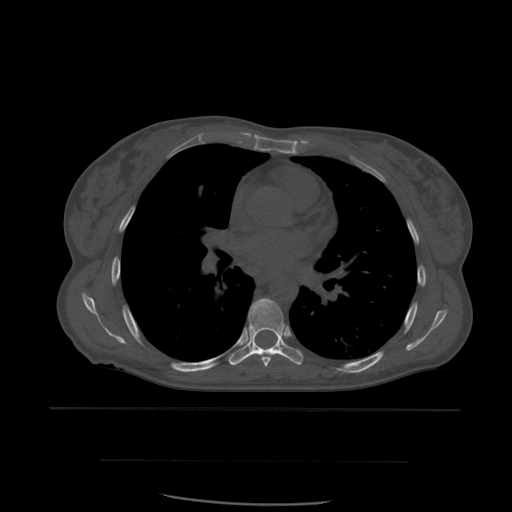
CT including the spine, one axial slice; bone window (W 1800 / L 400 HU); 512 × 512 image matrix, field of view 392 × 392 mm. Patient age 48 years. From the clinical record (not read from this slice): primary cancer: lung; vertebrae with lytic lesions (as recorded): T11.
Outlined on this slice (semi-automatically segmented with operator editing):
- T6 vertebra: box from (x=260, y=354) to (x=273, y=368) px
- T7 vertebra: (x=229, y=299)–(x=303, y=366)